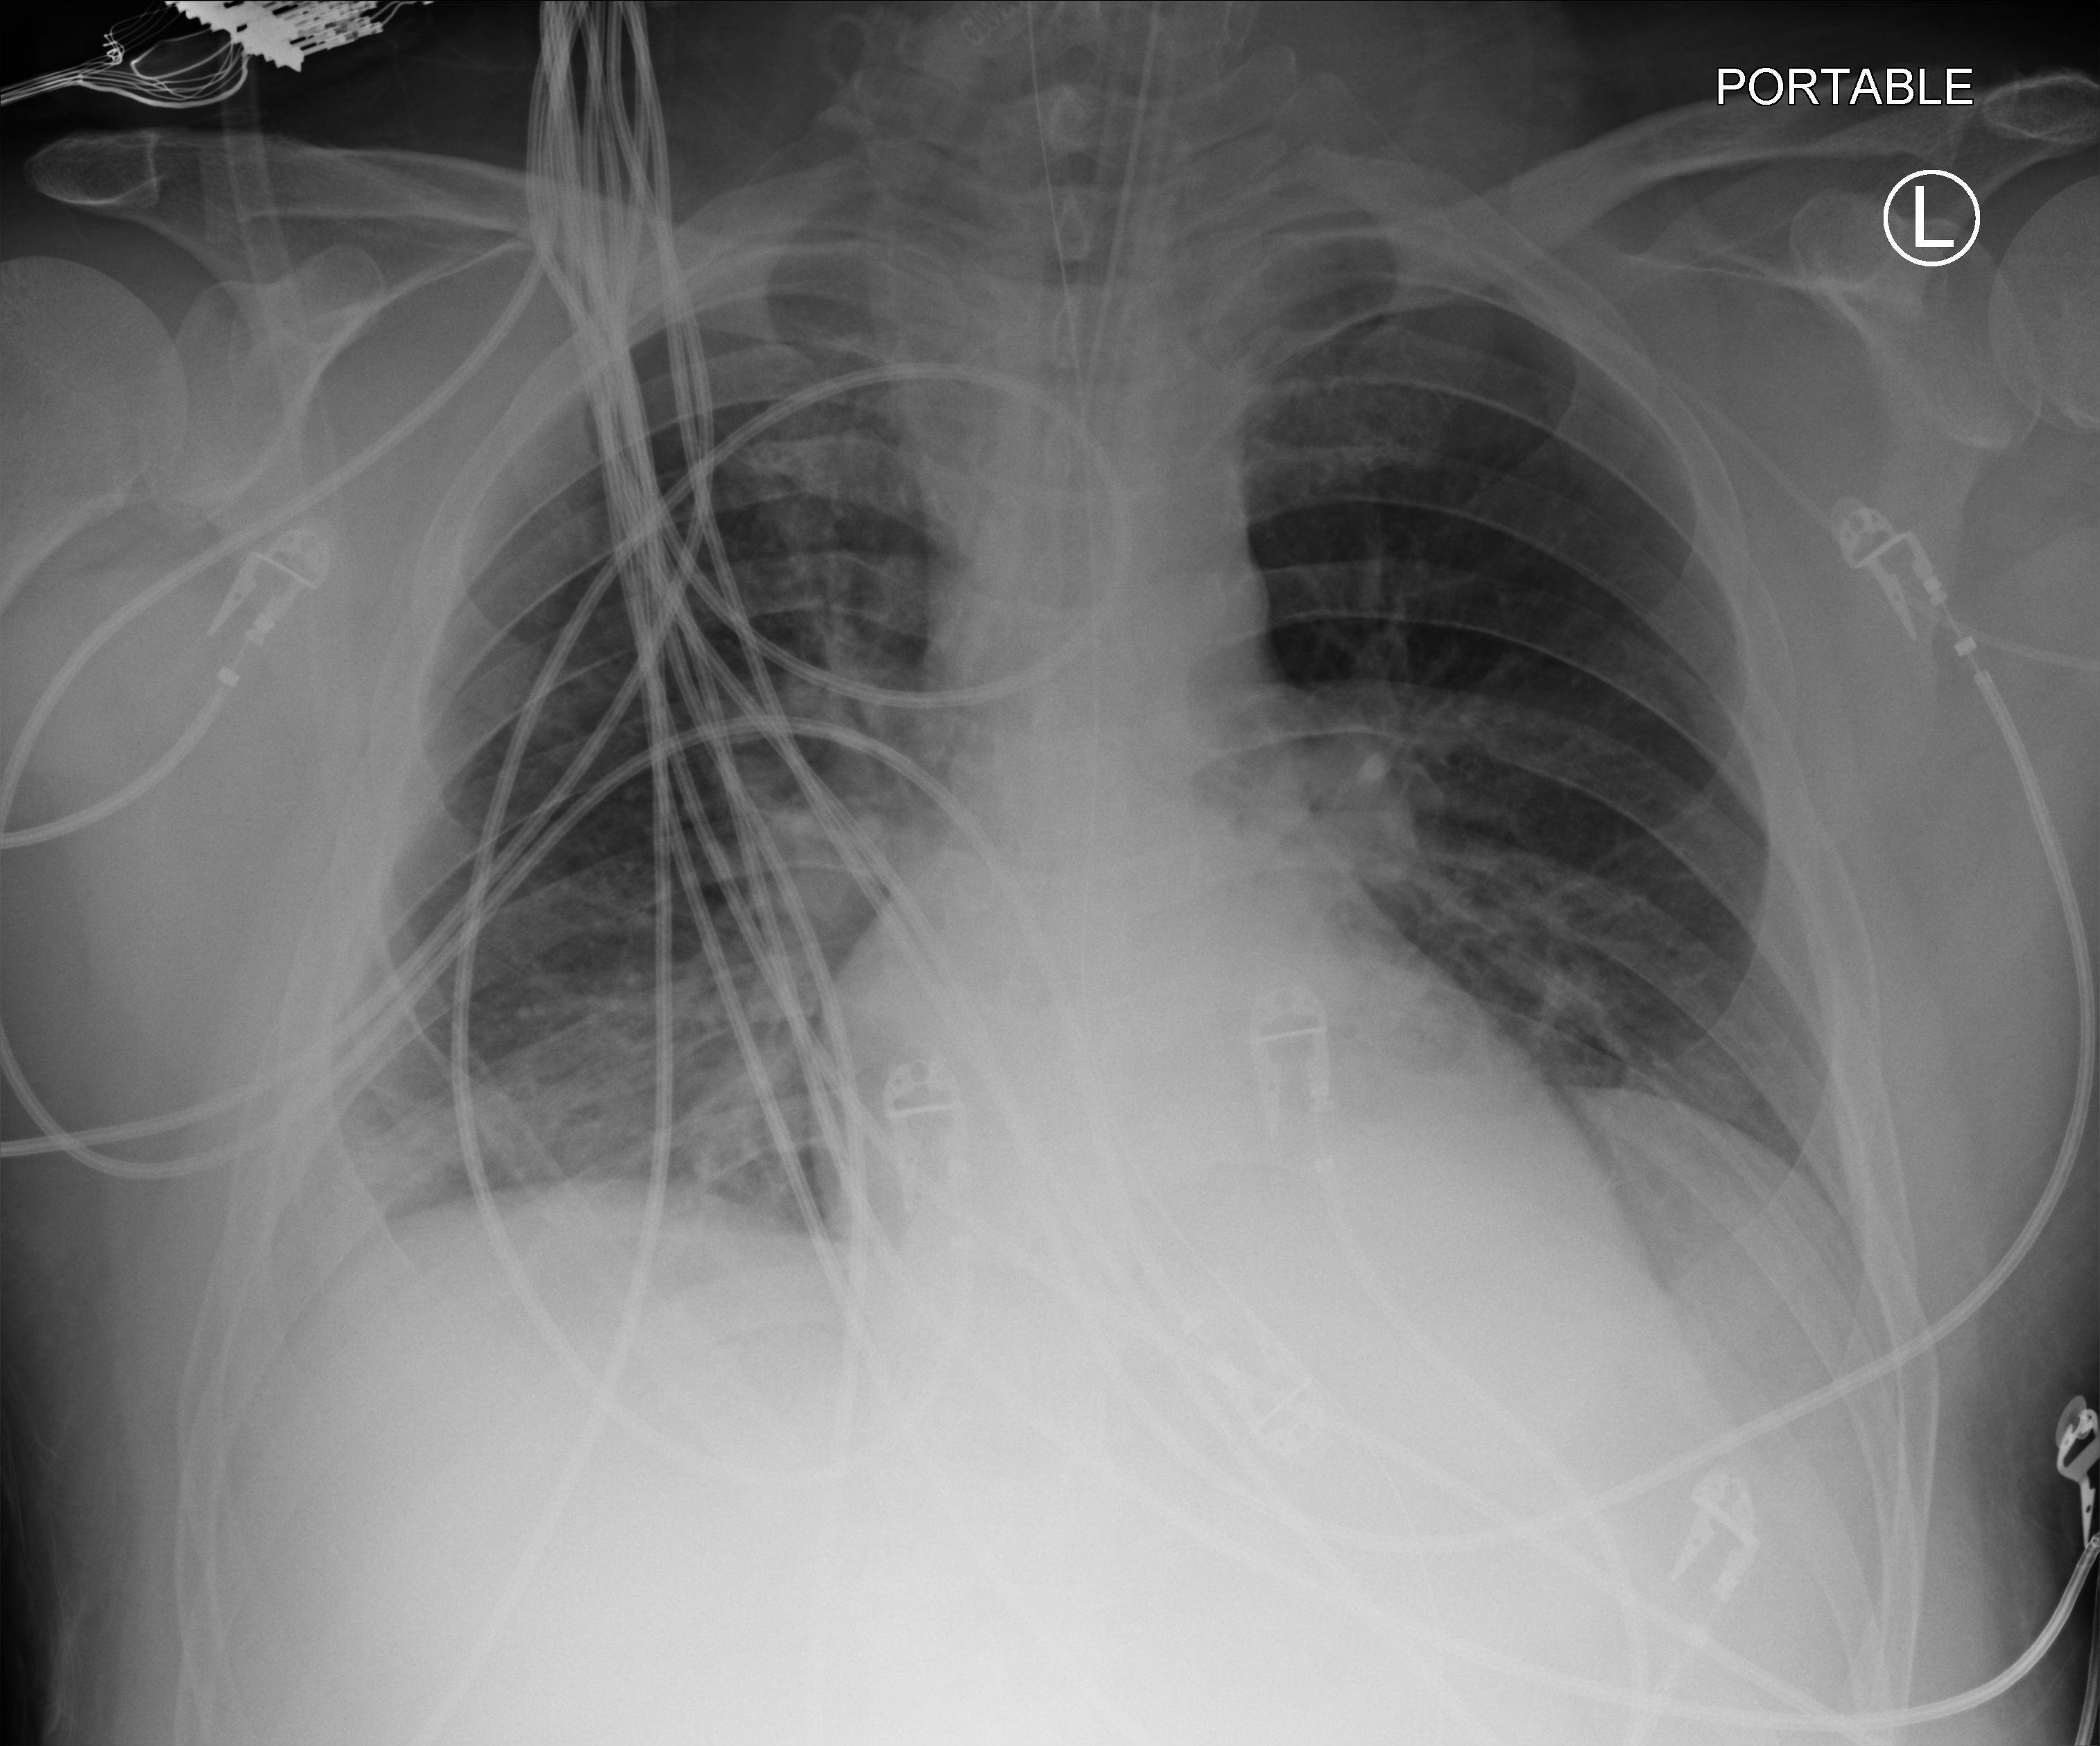
Bedside chest radiograph (computed radiography); anteroposterior (AP) projection. Male patient hospitalised with COVID-19, age 18–59 years.
From the hospital-stay record, not from the radiograph (when in the stay this image was taken is not recorded): mechanically ventilated during this hospital stay: yes; admitted to intensive care during this hospital stay: yes.